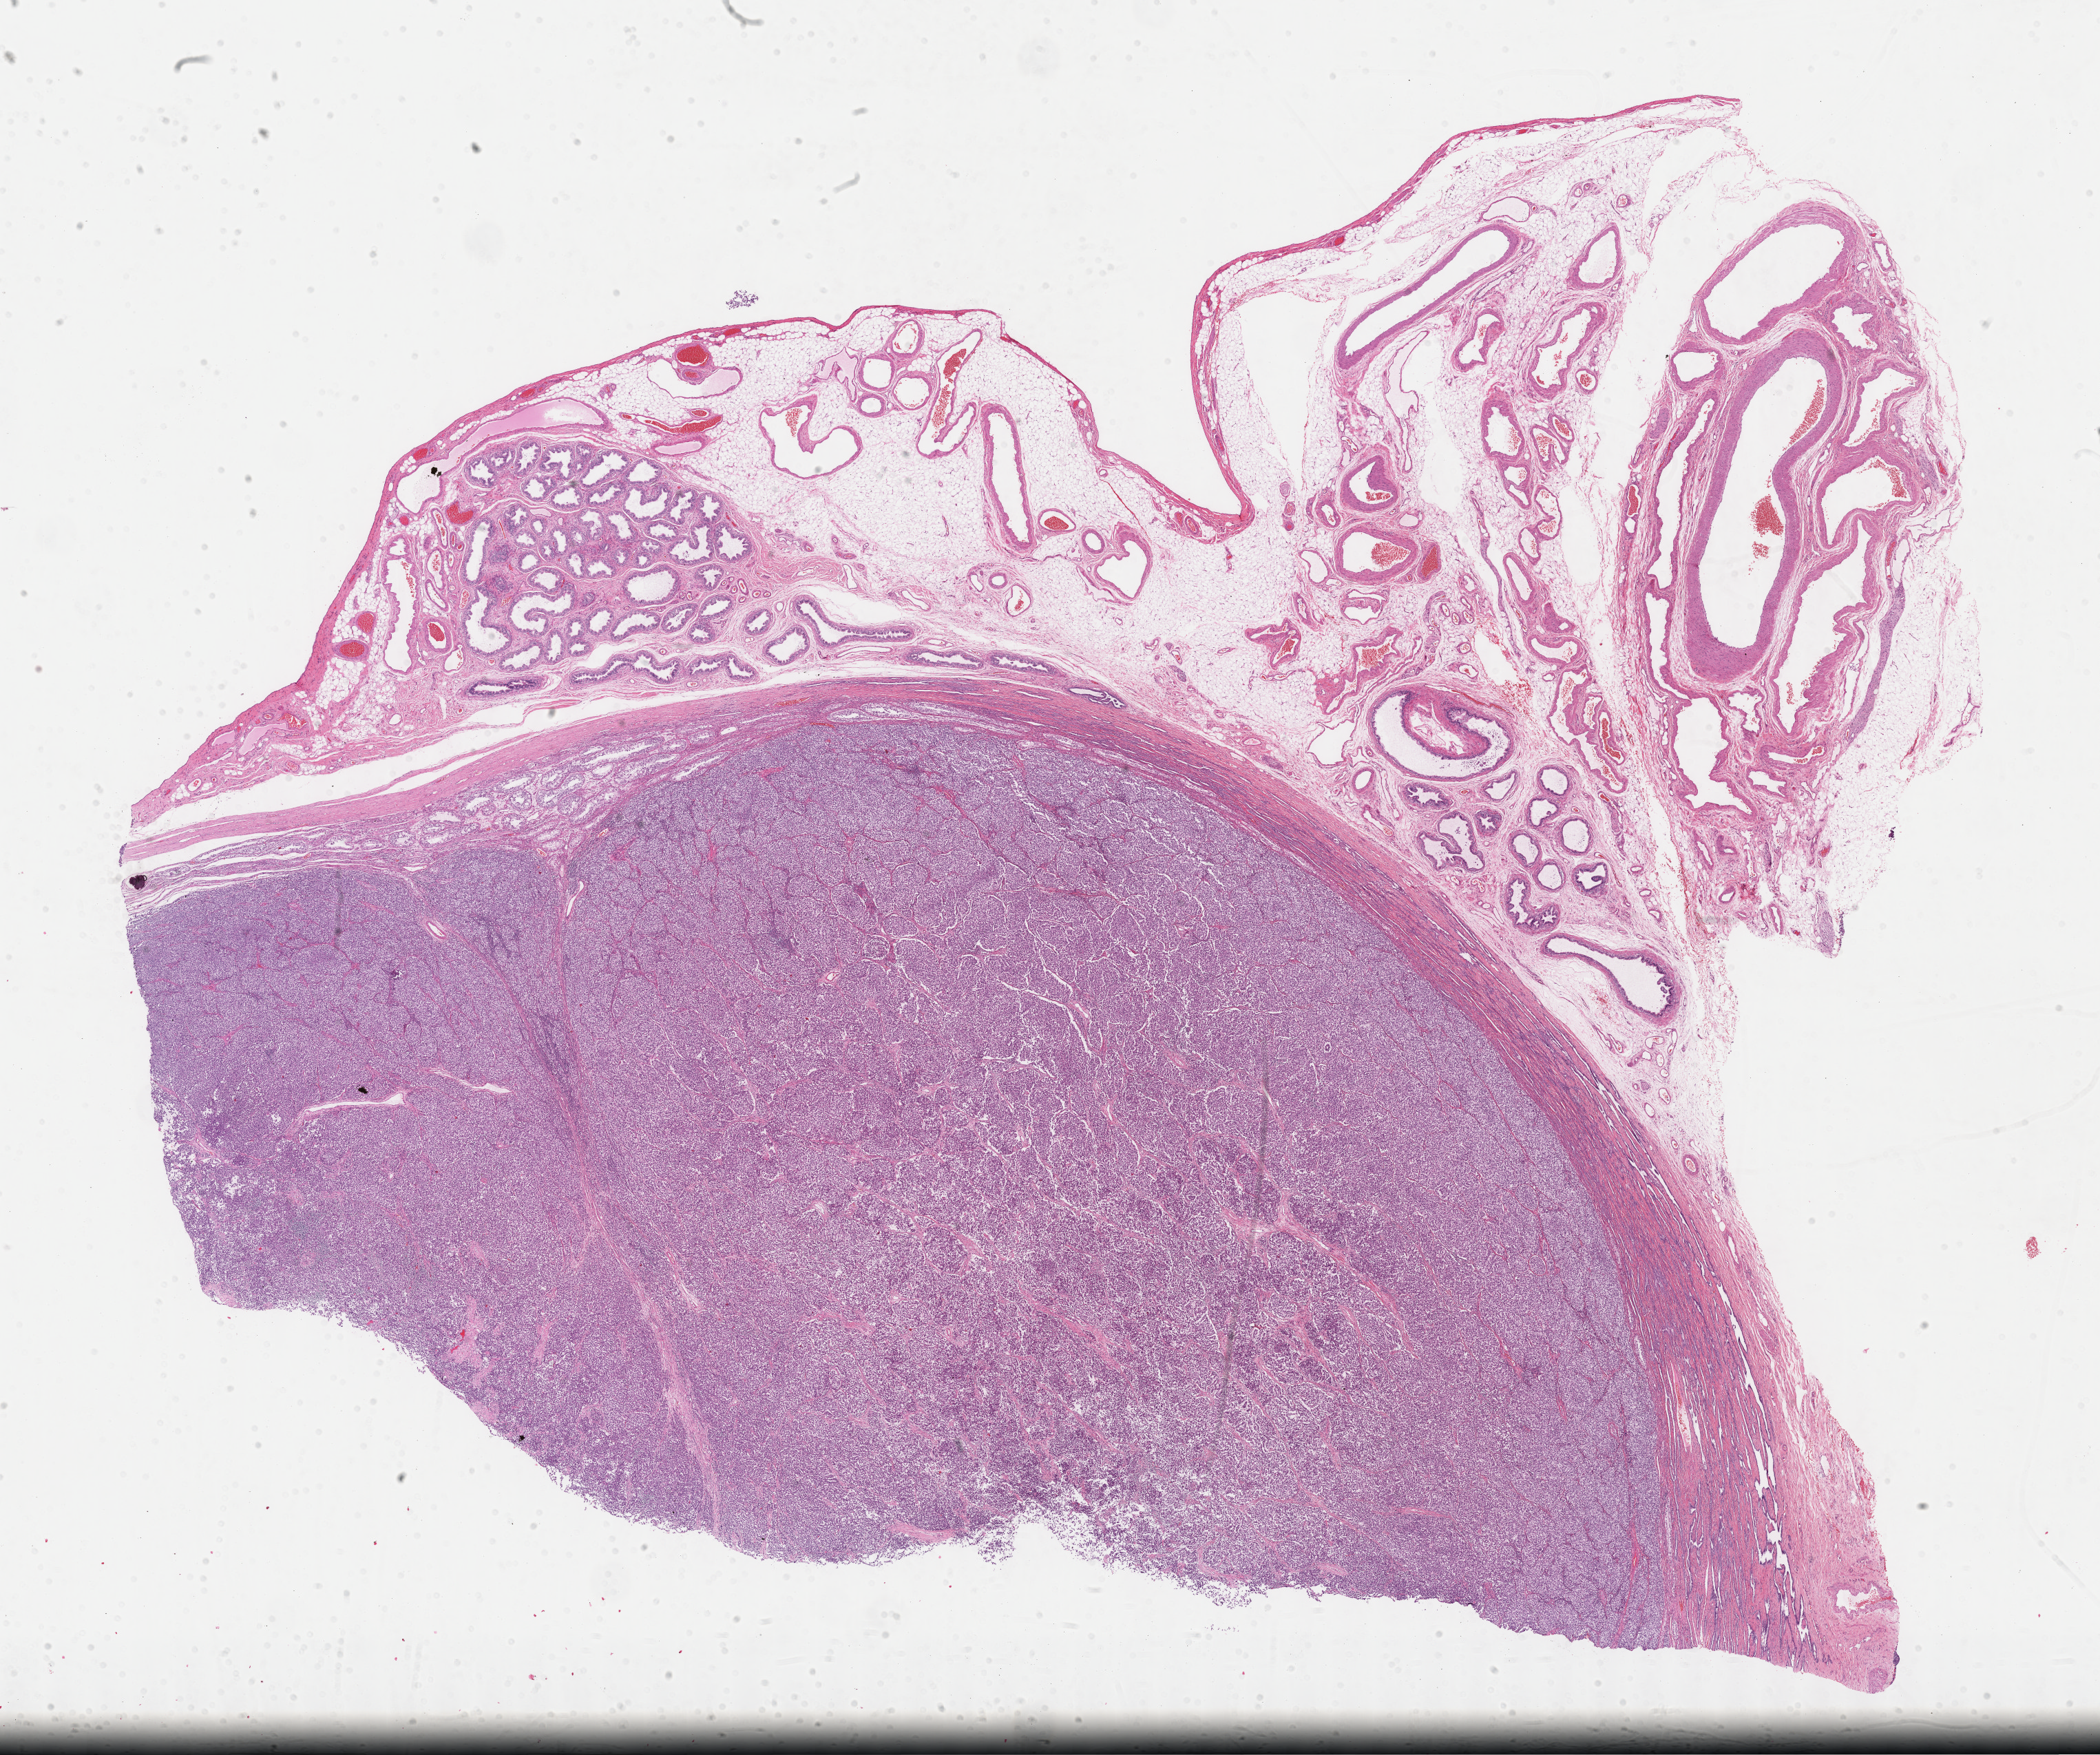
Digitized H&E-stained tissue section (whole slide), whole scanned area (about 24.7 x 20.6 mm) shown as a low-resolution overview. Formalin-fixed paraffin-embedded (FFPE) diagnostic section. Sample: primary tumour, testis. Male, age 38 years at initial diagnosis.
Pathologic diagnosis: Seminoma, NOS.